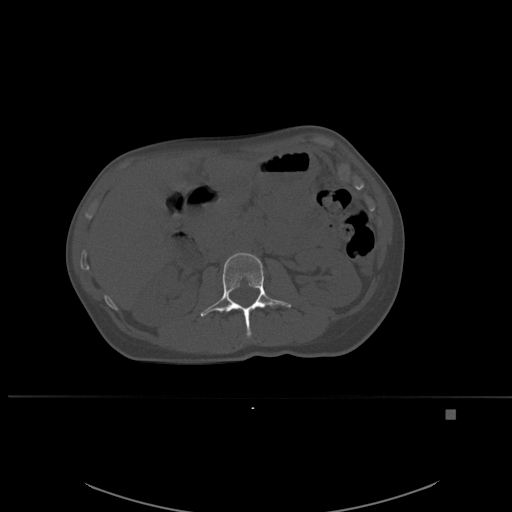
CT including the spine, one axial slice. Slice 238 of 537 in the series (ordered by position). Bone window (W 1800 / L 400 HU). 1.5 mm slice thickness. 512 × 512 image matrix. Patient: female, 45 years. Case-level facts recorded for this patient, not image findings: primary cancer: lung.
Structures marked on this image (semi-automatically segmented with operator editing):
- L2 vertebra: bounding box (x1, y1, x2, y2) in pixels: (200, 252, 292, 338)